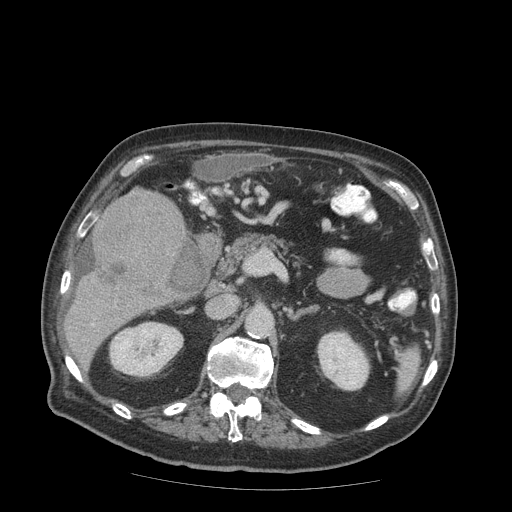
Contrast-enhanced abdominal CT (liver protocol), one axial slice; slice 36 of 99 in the series (ordered by position); reconstruction kernel STANDARD; 140 kVp; soft-tissue window (W 400 / L 40 HU); 512 × 512 image matrix, field of view 420 × 420 mm. From the clinical record (not read from this slice): diagnosis: hepatocellular carcinoma (patient treated with transarterial chemoembolisation; whether this scan precedes or follows treatment is not stated here); TNM stage (as recorded): Stage-IIIB; Child-Pugh class: A; tumour differentiation: well differentiated; tumour nodularity: multinodular.
Structures marked on this image (semi-automatic segmentation, software-assisted and operator-edited):
- liver parenchyma outside the tumour (the mass and vessels are separate outlines, so this box may not span the whole liver): box from (x=64, y=223) to (x=186, y=345) px
- mass: (x=90, y=186)–(x=186, y=299)
- liver vessels: (x=91, y=323)–(x=94, y=326)